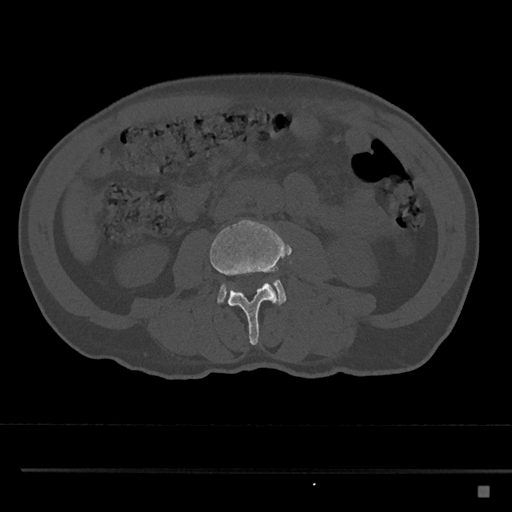
CT including the spine, one axial slice; slice 680 of 797 in the series (ordered by position); bone window (W 1800 / L 400 HU); 0.5 mm slice thickness; 512 × 512 image matrix. Patient: male, 59 years. From the clinical record (not read from this slice): primary cancer: prostate.
Annotated regions visible in this slice (semi-automatic segmentation, software-assisted and operator-edited):
- L3 vertebra: bounding box <209,219,287,345> (left, top, right, bottom; pixels)
- L4 vertebra: <217,279,287,305>